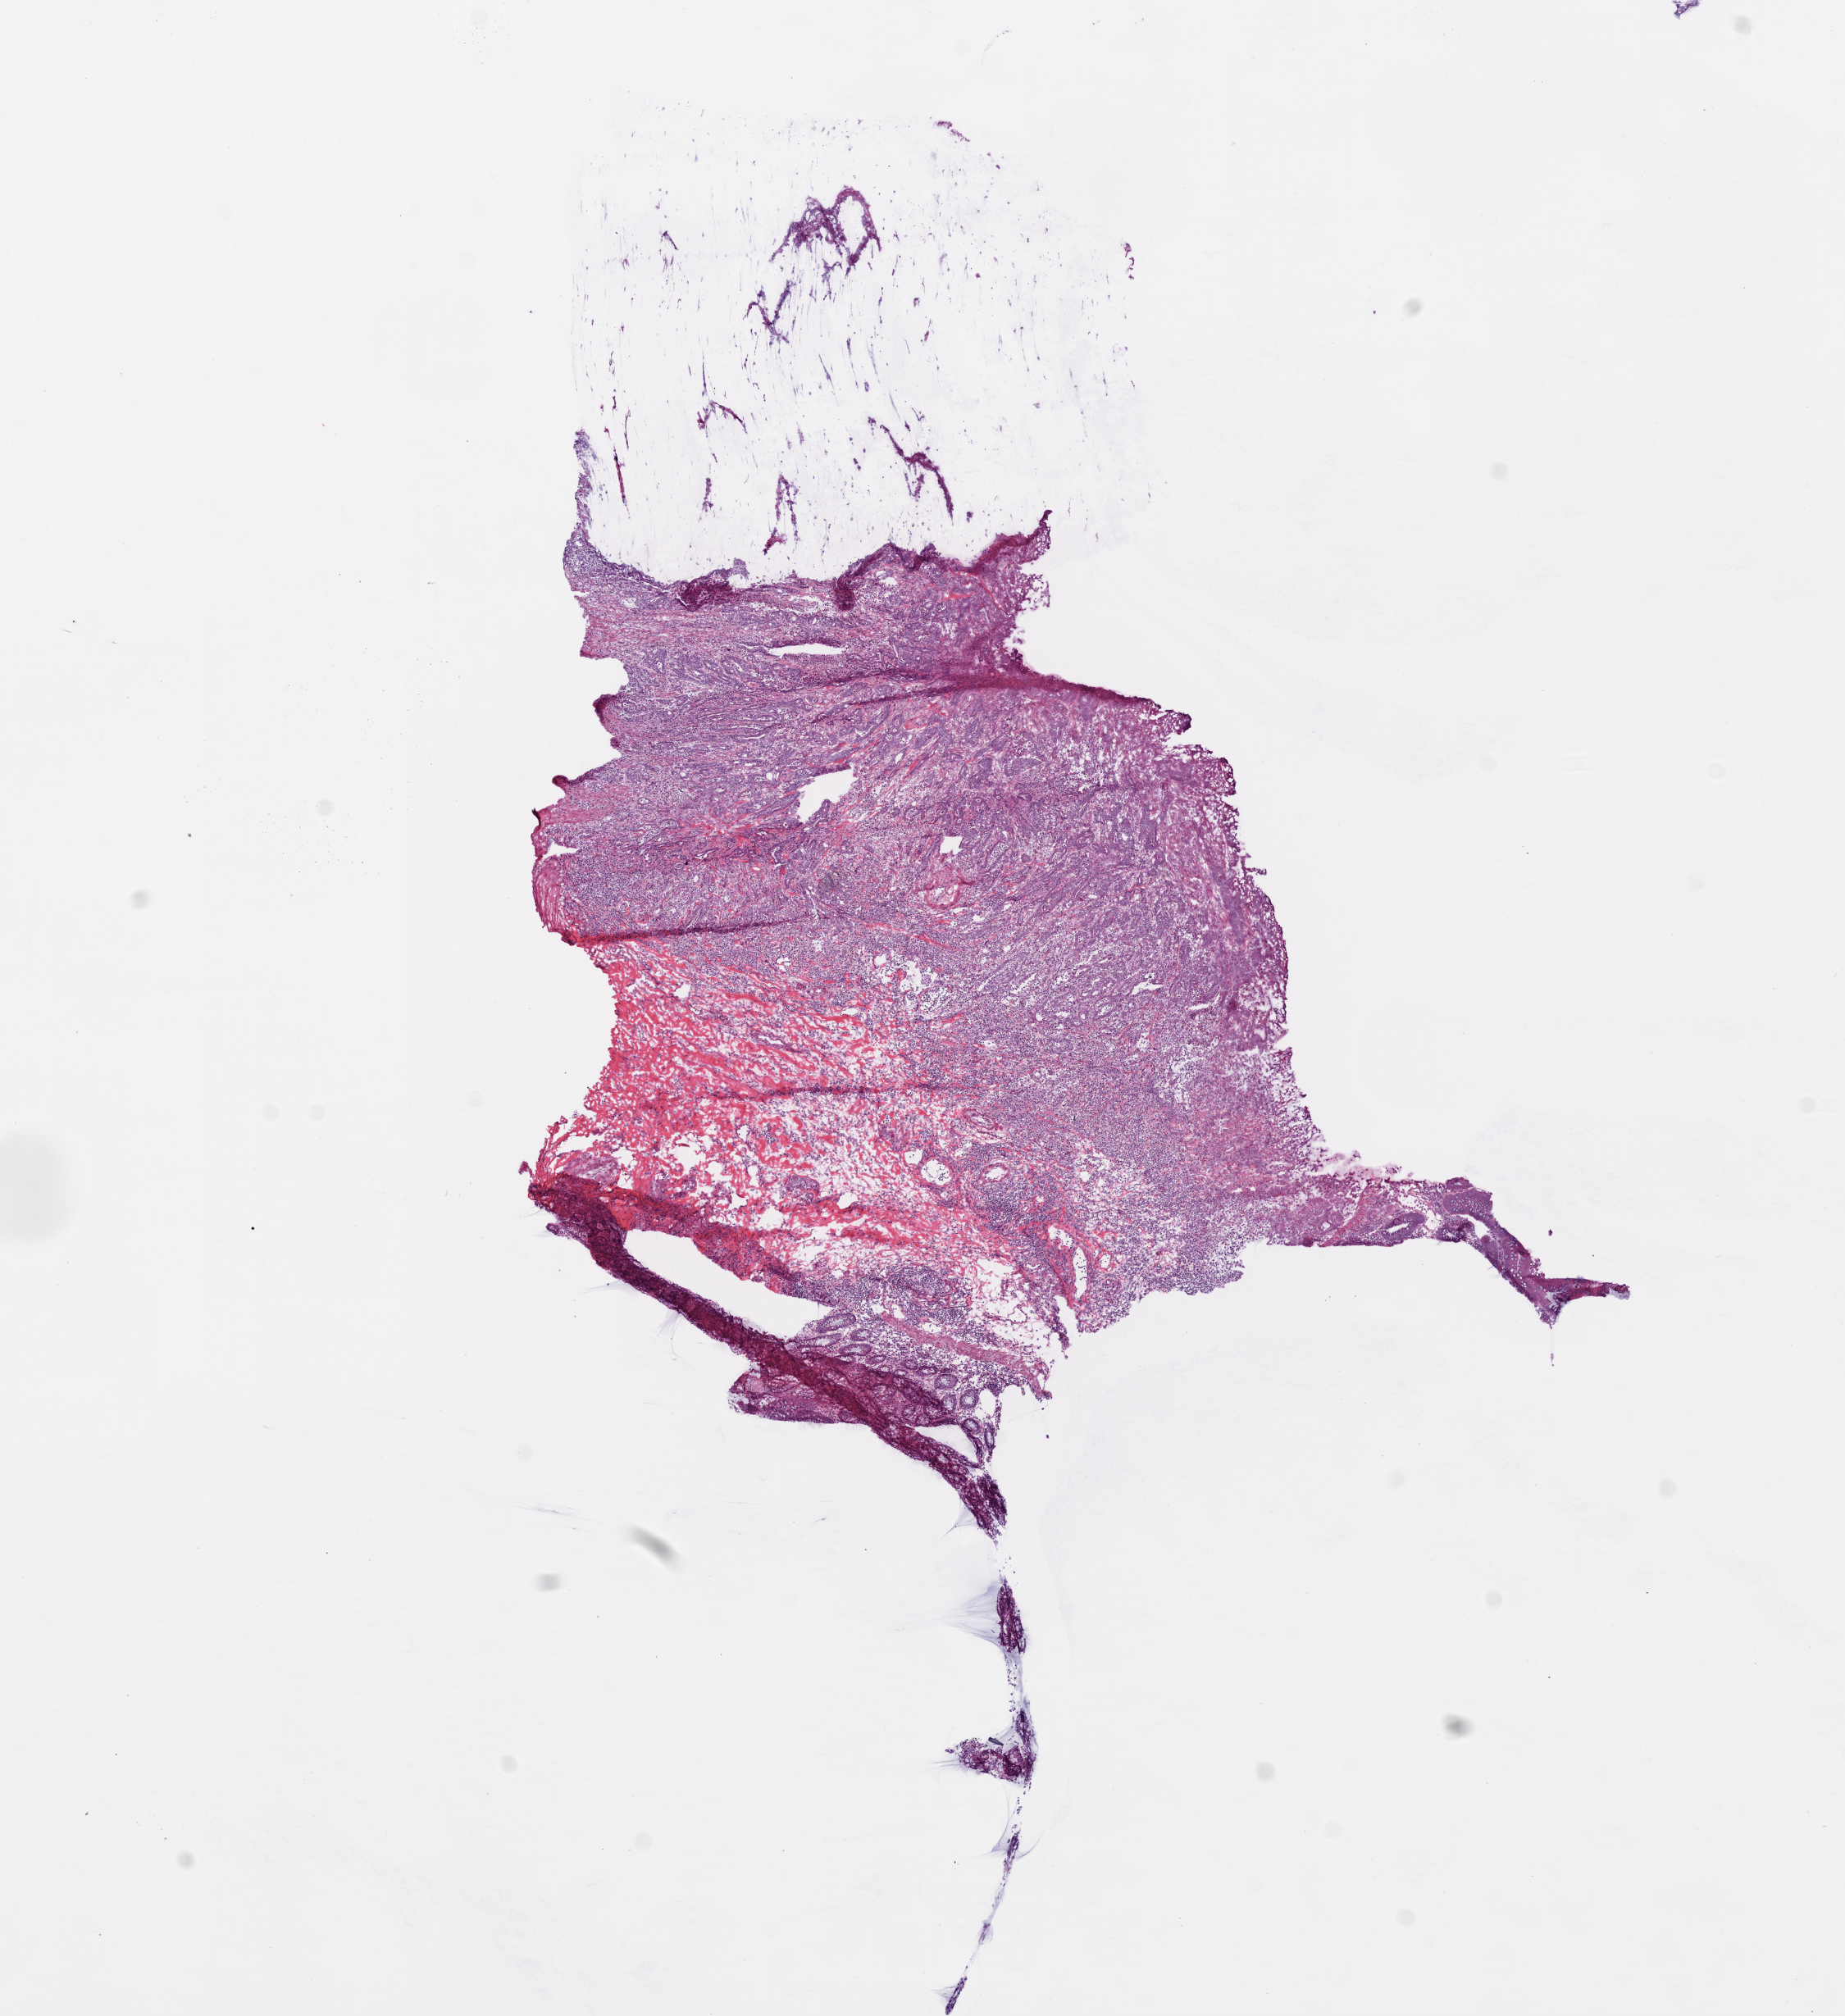
H&E-stained whole-slide image, whole scanned area (about 9.0 x 9.9 mm, slide scanned at 20x) shown as a low-resolution overview, frozen section from the top of the tissue portion, sample: primary tumour, colon. Female, age 63 years at initial diagnosis. Slide review estimates, as recorded: tumour cells 80%, tumour nuclei 70%, normal cells 5%, stromal cells 15%, necrosis 5%.
• AJCC pathologic stage: IIA (6th edition)
• pathologic diagnosis: Adenocarcinoma, NOS
• TNM: T3 N0 M0
• lymph nodes positive (case pathology): 0 of 12 examined